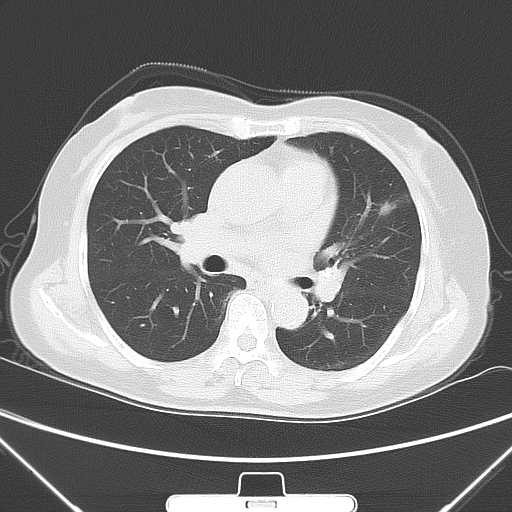
Chest CT, one axial slice; position 31 of 60 along the scan axis; lung window (W 1500 / L -600 HU); 512 × 512 image matrix. Female patient, age 70 years. Case-level facts recorded for this patient, not image findings: clinical TNM (as recorded): T1b N0 M0.
Annotated regions visible in this slice (rectangle marked by the reading radiologist):
- lung tumour (recorded histology: adenocarcinoma): box from (x=365, y=189) to (x=399, y=224) px